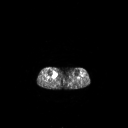
FDG PET of an extremity soft-tissue mass (from a PET/CT study), one axial slice. 3.27 mm slice thickness. 128 × 128 image matrix. Patient: female, 65 years. From the clinical record (not read from this slice): histological type: undifferentiated – high grade; grade: high; site of the primary tumour: right thigh.
Structures marked on this image (expert contour drawn on MRI and transferred to this co-registered scan by the dataset authors):
- gross tumour volume (mass): bounding box <52,71,57,77> (left, top, right, bottom; pixels)